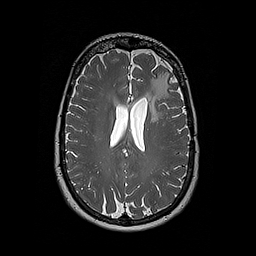
Brain MRI from a brain-tumour surgery series, one axial slice. Slice 116 of 192 in the series (ordered by position). 1 mm slice thickness. 256 × 256 image matrix, field of view 250 × 250 mm. Case-level facts recorded for this patient, not image findings: histopathology: Oligodendroglioma; WHO grade: 2; IDH mutation: yes.
Structures marked on this image (manually delineated by an expert):
- tumour: bounding box [x1, y1, x2, y2] px = [146, 76, 161, 121]